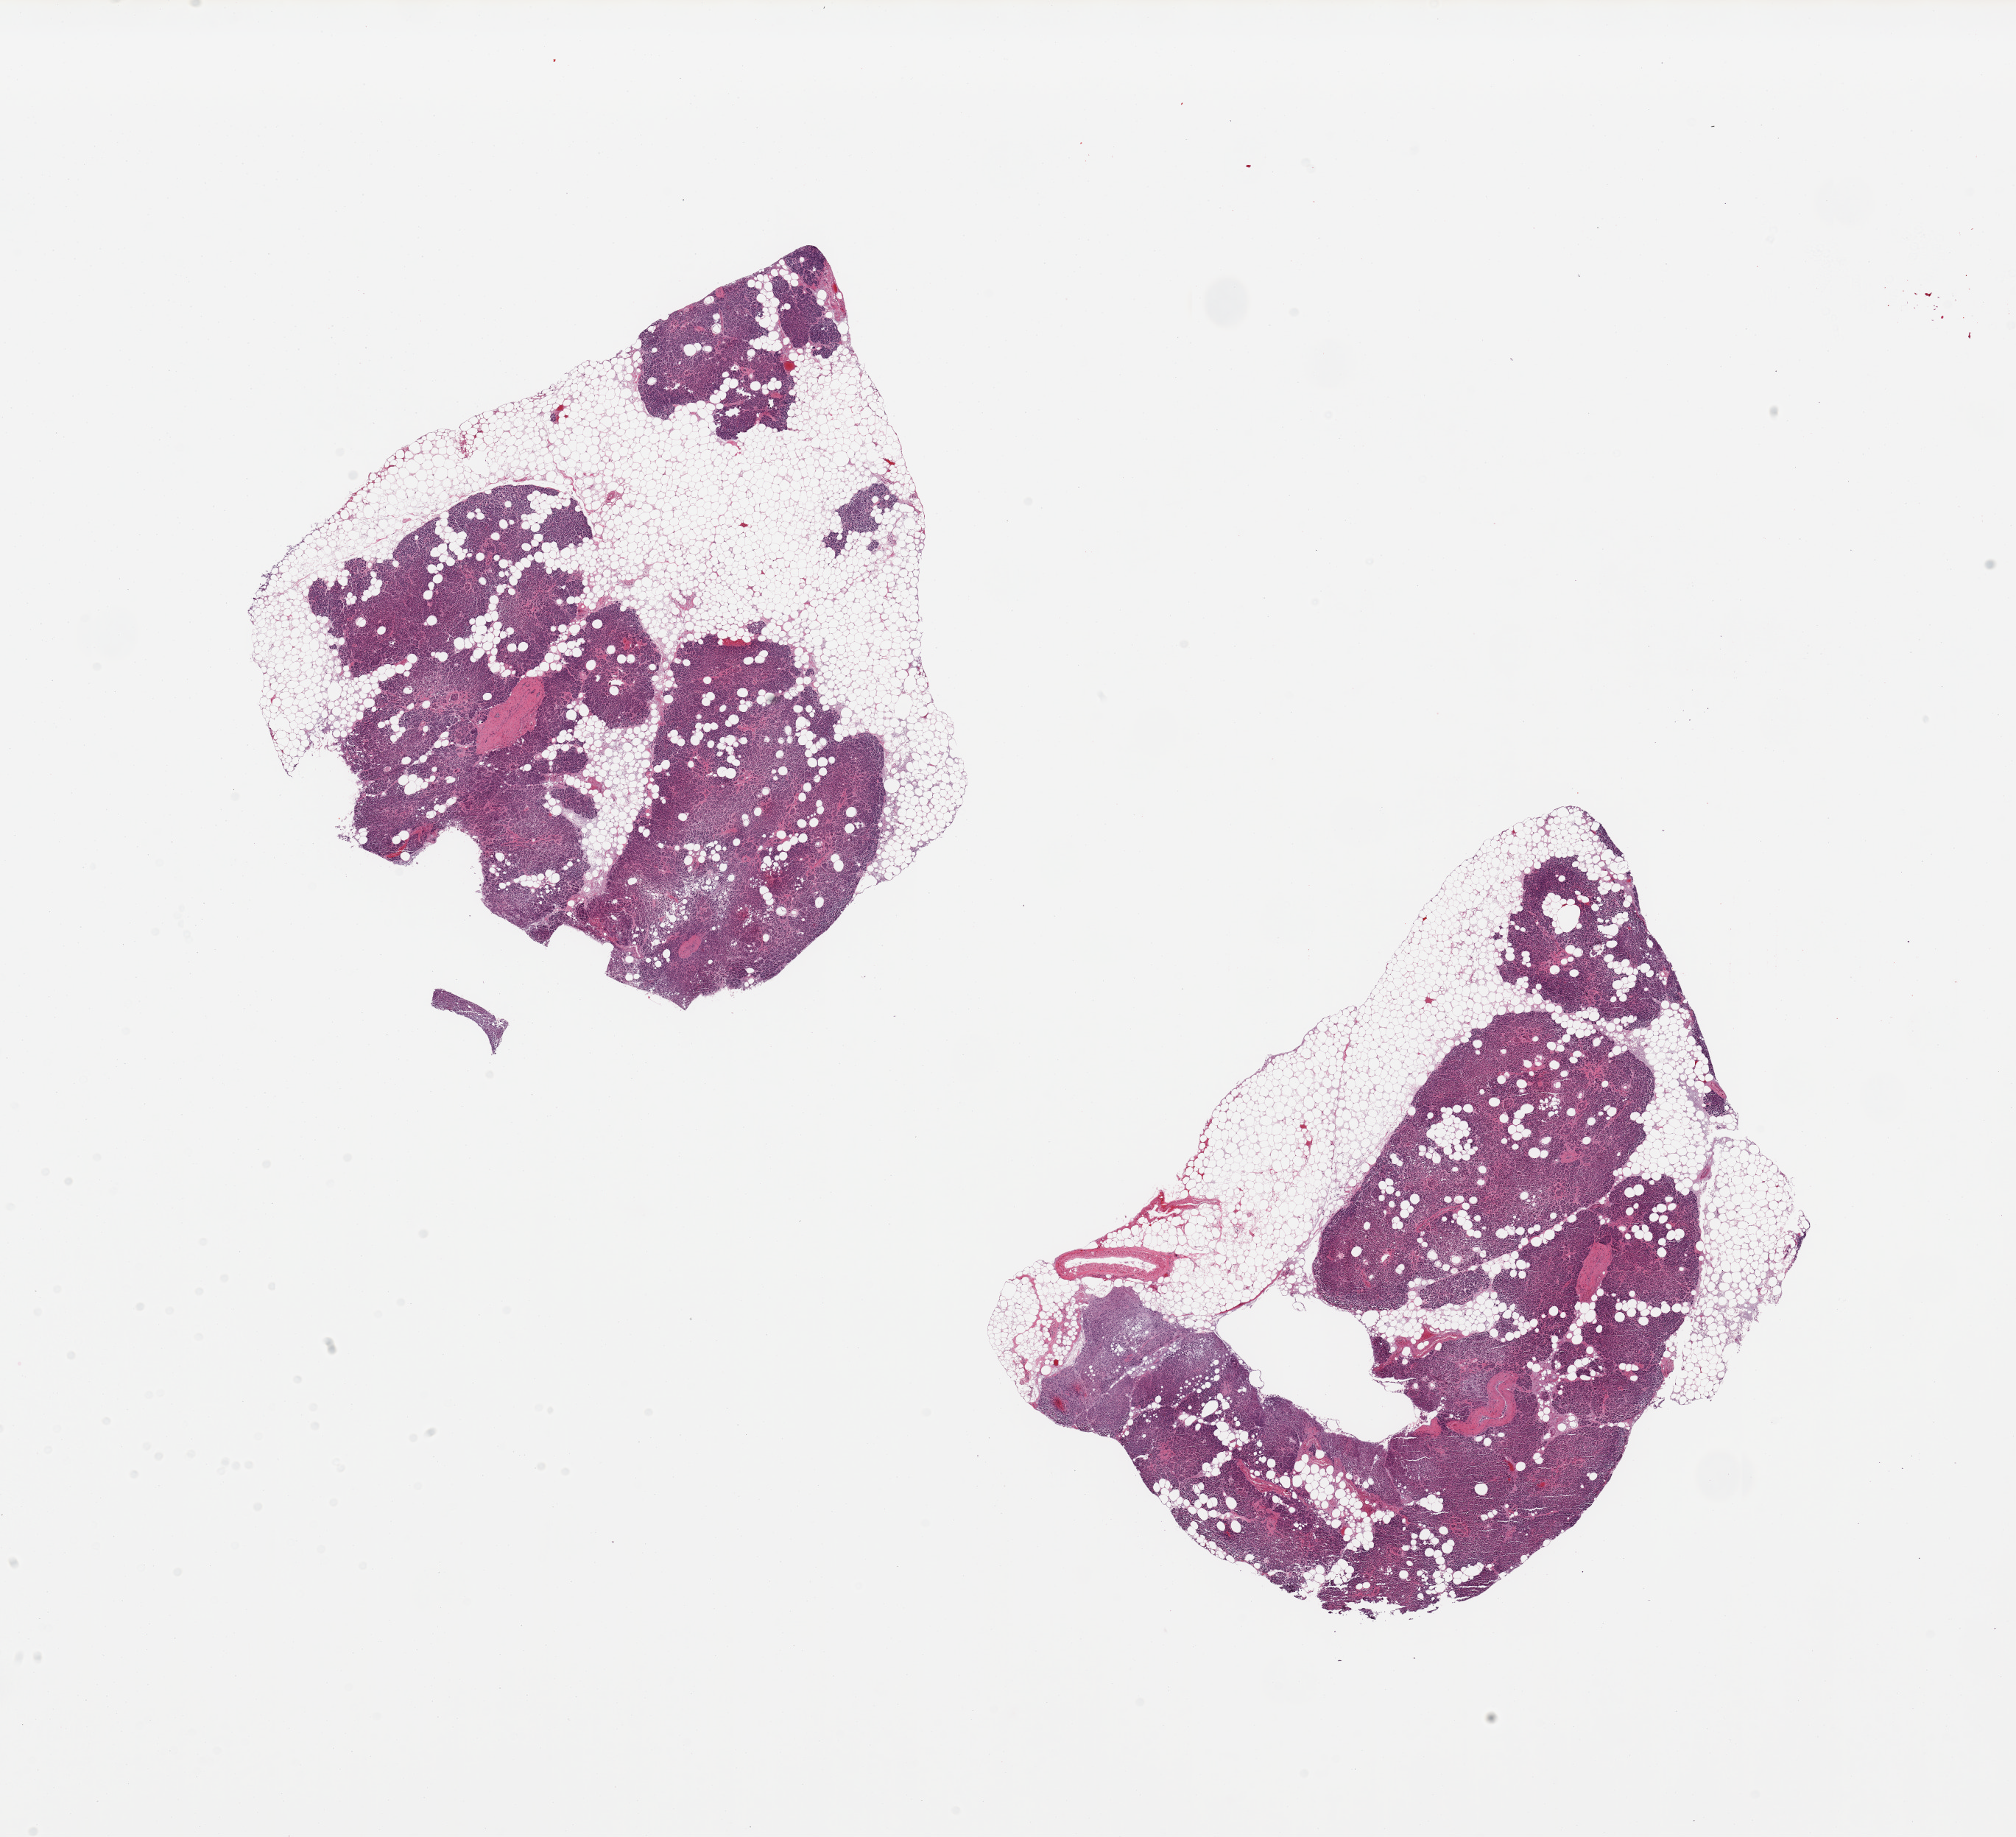
Whole-slide image, H&E stain, low-resolution overview of the scanned area, about 21.7 x 19.7 mm (from a 20x scan), PAXgene-fixed paraffin-embedded (PFPE) section, sampled site (target tissue): pancreas, donor tissue sample. Donor sex: female.
Pathologist's review note for this sample: 2 pieces; includes 30-50% internal and attached fat, few residual islets.